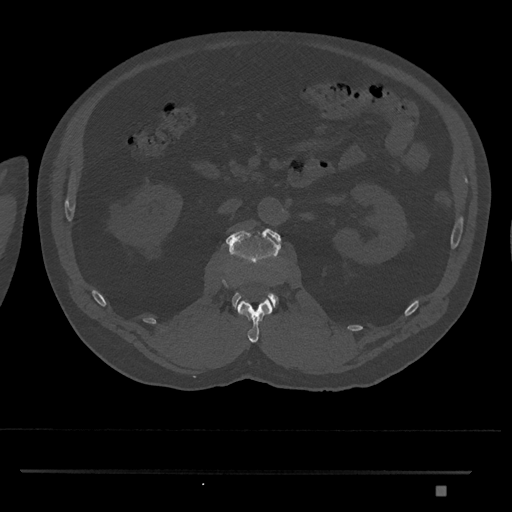
CT including the spine, one axial slice. Position 791 of 1134 along the scan axis. Reconstruction kernel Br40s/3. Bone window (W 1800 / L 400 HU). 0.5 mm slice thickness. 512 × 512 image matrix, field of view 429 × 429 mm. Male patient, age 65 years. From the clinical record (not read from this slice): primary cancer: prostate.
Annotated regions visible in this slice (semi-automatically segmented with operator editing):
- L1 vertebra: bounding box [x1, y1, x2, y2] px = [237, 298, 273, 343]
- L2 vertebra: [226, 228, 281, 310]